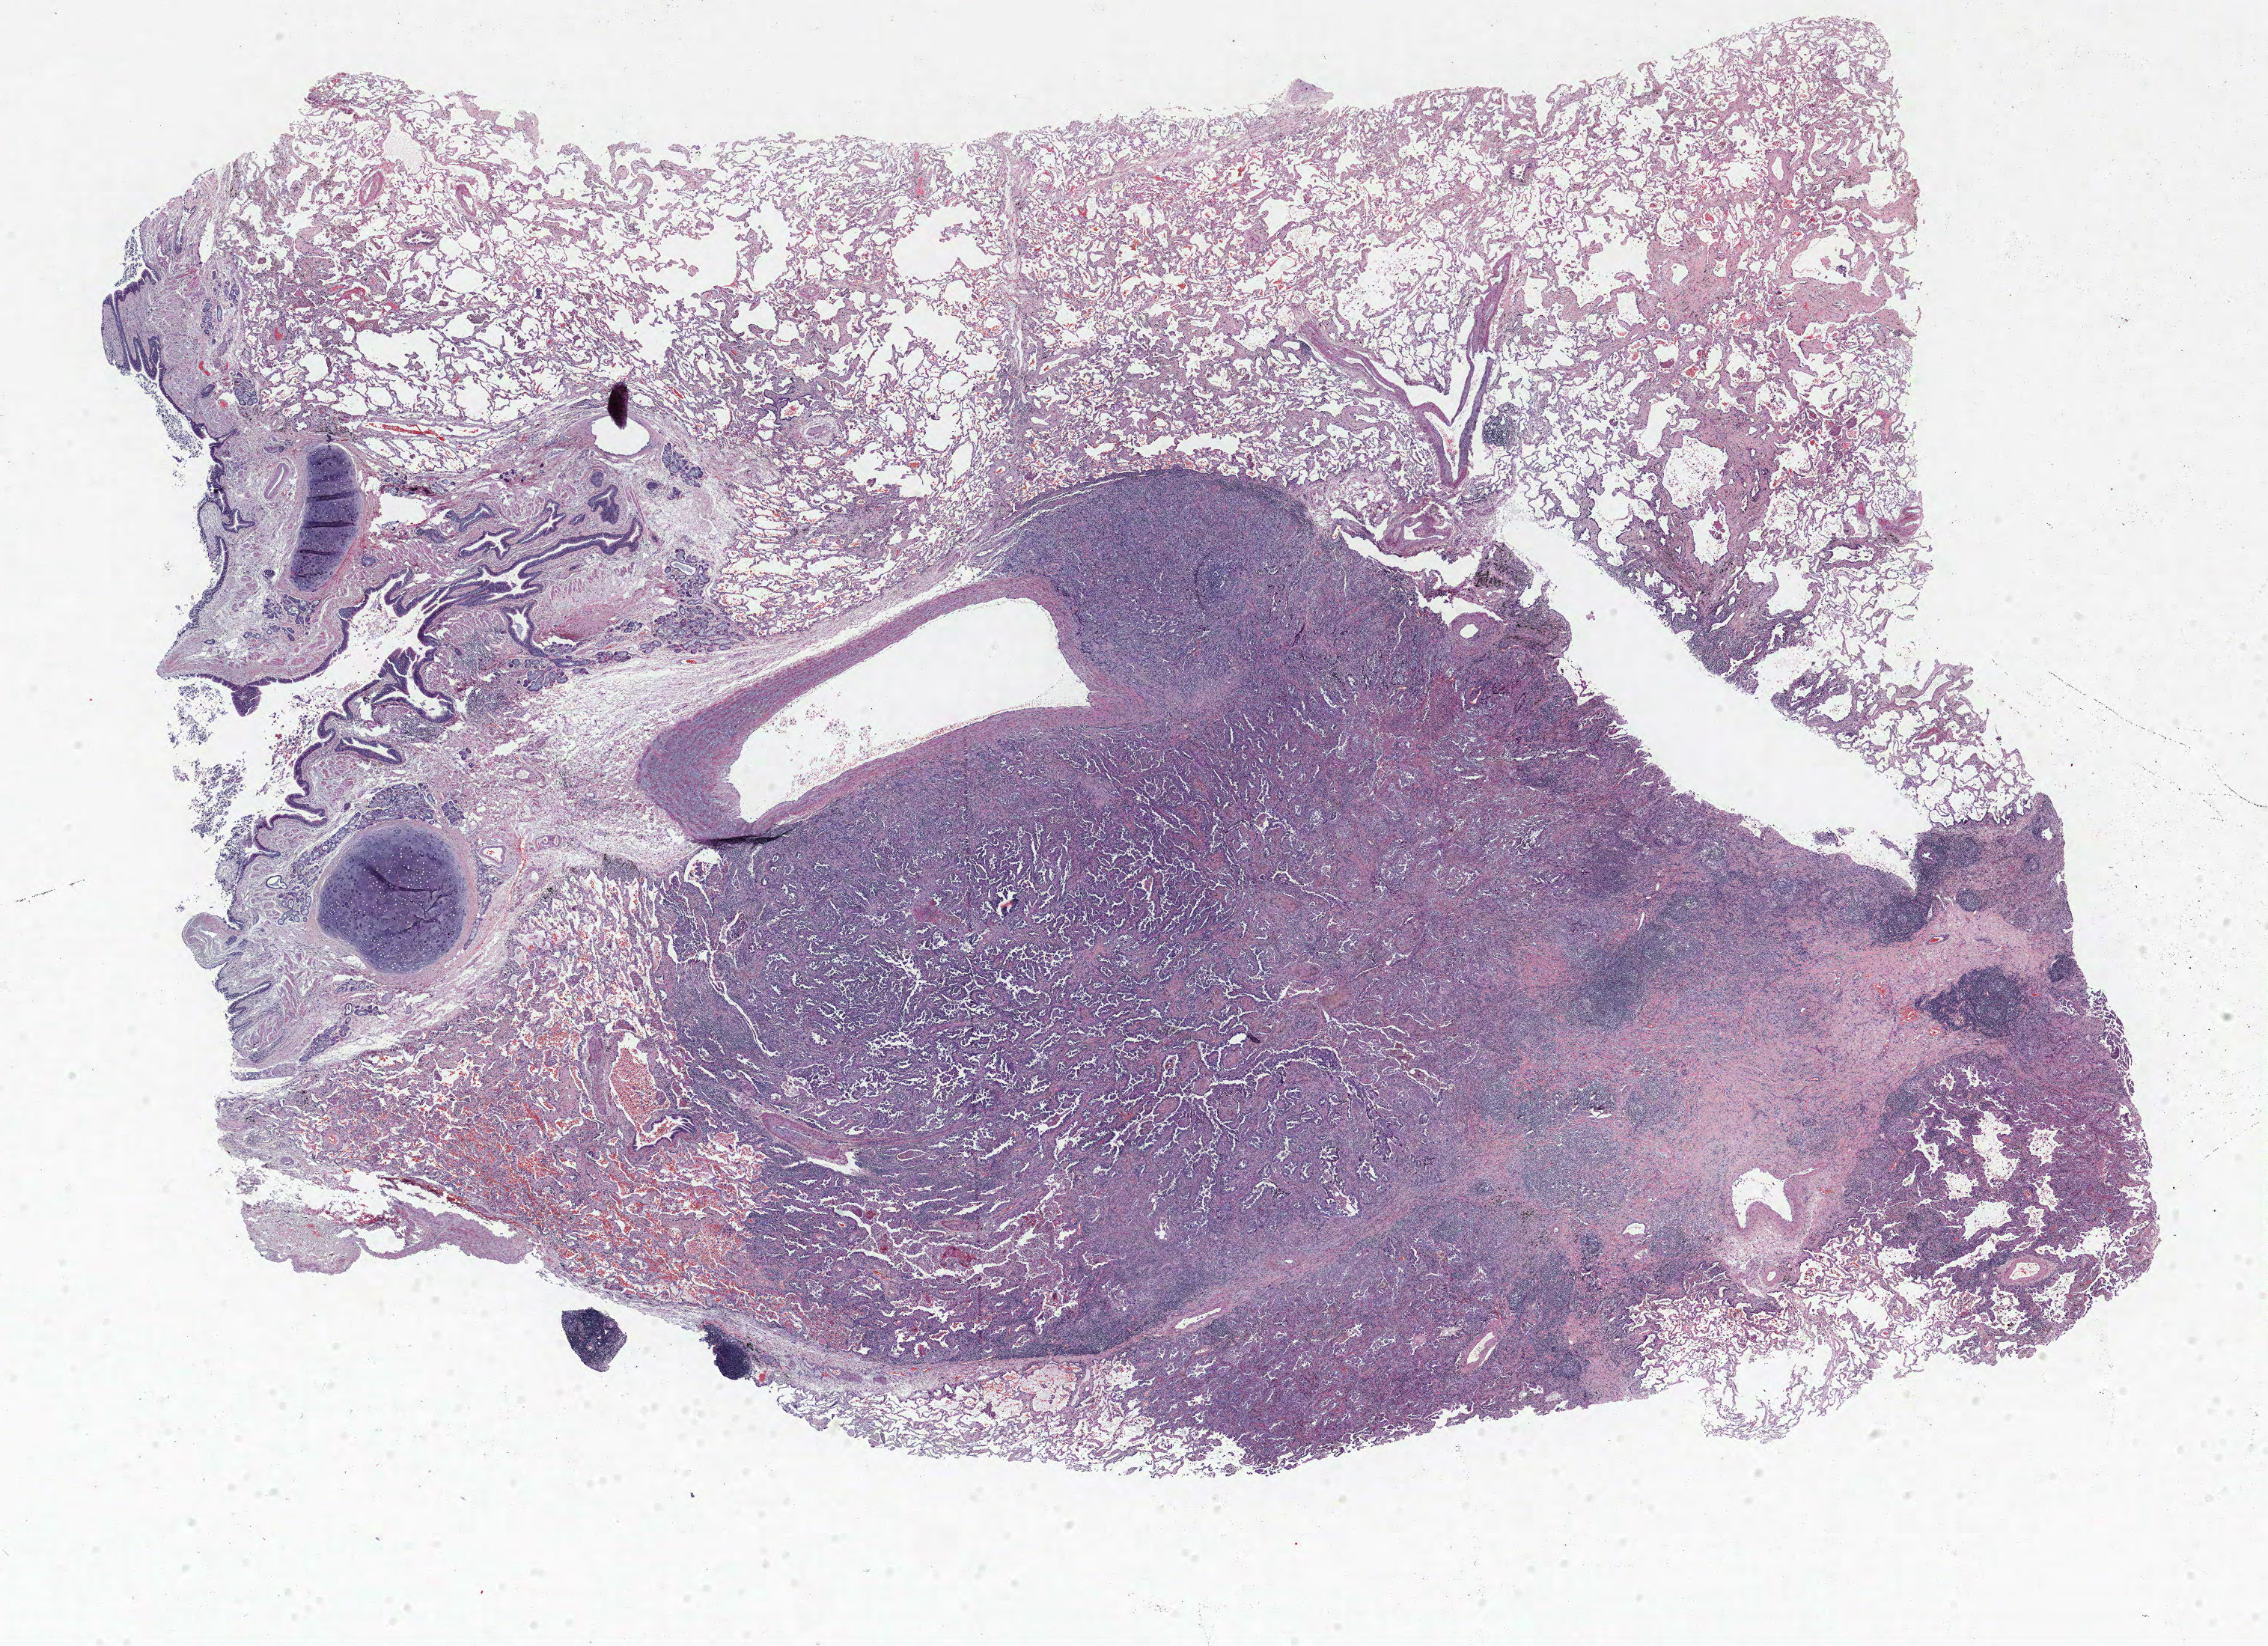
Whole-slide histology image, H&E-stained — whole scanned area (about 24.2 x 17.6 mm, slide scanned at 40x) shown as a low-resolution overview. Formalin-fixed paraffin-embedded (FFPE) section. Lung. Female patient, aged 66 at enrolment. Current smoker at enrolment. Grade: poorly differentiated (G3).
Primary tumour location (clinical record): right upper lobe. Tumour size (pathology): 18 mm. Participant's lung-cancer diagnosis: Adenocarcinoma, NOS. Stage (AJCC 6th edition): IA.